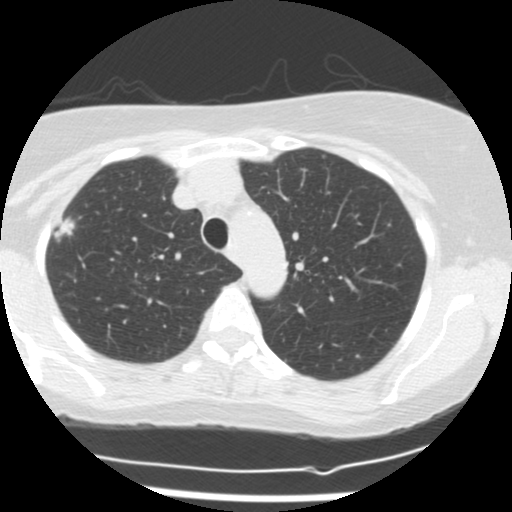
Axial slice from a low-dose chest CT screening exam; baseline annual screen; lung window (W 1500 / L -600 HU); 2.5 mm slice thickness; 120 kVp; slice 41 of 160 in the series. Female participant, aged 58 years at enrolment. Former smoker at enrolment.
Expert reader's lesion annotation, bounding box <44,205,89,242> (left, top, right, bottom; pixels). Screening reader's record for this exam (one nodule recorded; not confirmed to be the boxed lesion): non-calcified nodule or mass ≥4 mm, right upper lobe, 12 × 9 mm, spiculated (stellate) margins, soft tissue attenuation. Official screen result: positive, change unspecified: nodule(s) >= 4 mm or enlarging nodule(s), mass(es), or other non-specific abnormalities suspicious for lung cancer. Later outcome: lung cancer diagnosed 21 days after this screen — adenocarcinoma, NOS, right upper lobe, moderately differentiated (G2), stage IA (AJCC 6th edition), 10 mm at pathology.